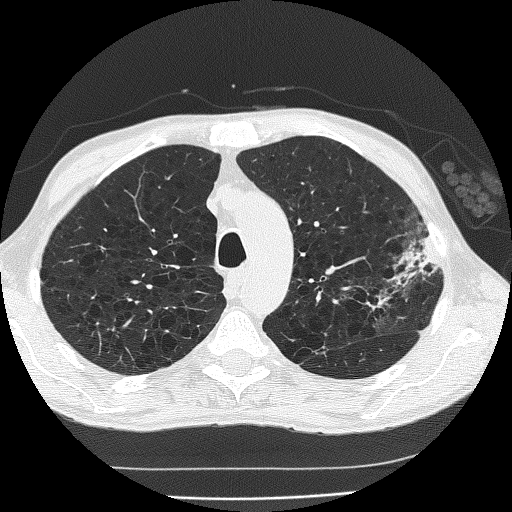
Low-dose screening chest CT, axial slice. Second screening round (one year after baseline). Lung window (W 1500 / L -600 HU). Lung (sharp) reconstruction kernel (FC51). 120 kVp. Slice 47 of 185 in the series. 512 × 512 image matrix. Male, age 60 years at enrolment. Current smoker at enrolment.
Lesion marked by an expert reader, bounding box <346,236,444,335> (left, top, right, bottom; pixels). The screening reader recorded 2 non-calcified nodules or masses ≥4 mm on this exam (left upper lobe, left upper lobe); which of them this box marks is not recorded. Official screen result: positive, other. Participant outcome: lung cancer diagnosed 178 days after this screen — bronchiolo-alveolar carcinoma, mucinous, left upper lobe, stage IV (AJCC 6th edition).